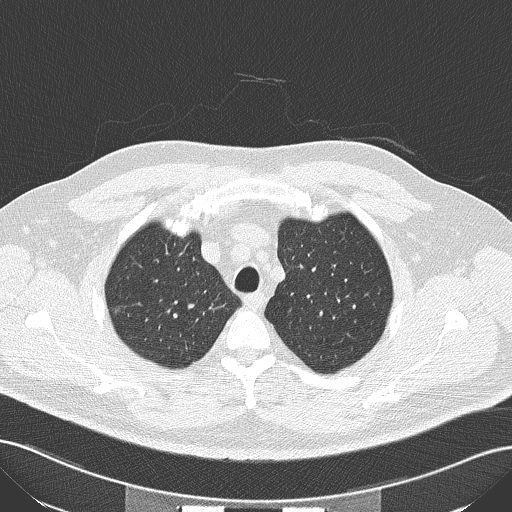
Axial slice from a low-dose chest CT screening exam. Second annual screen. Lung window (W 1500 / L -600 HU). 2 mm slice thickness. Slice 31 of 152 in the series. Male participant, aged 56 years at enrolment. Current smoker at enrolment.
Lesion marked by an expert reader, bounding box <95,293,142,332> (left, top, right, bottom; pixels). Reader record for this screening exam (exam-level; its link to the box is not recorded): non-calcified nodule or mass ≥4 mm, right upper lobe, 10 × 9 mm, spiculated (stellate) margins, soft tissue attenuation, pre-existing on the prior screen: no. Official screen result: positive, other.